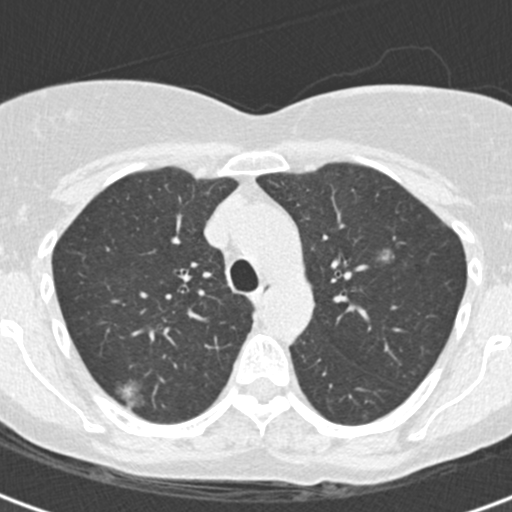
Low-dose screening chest CT, one axial slice. Position 126 of 172 along the scan axis. Lung window (W 1500 / L -600 HU). 2 mm slice thickness. 512 × 512 image matrix, field of view 283 × 283 mm.
Outlined on this slice (manually delineated by an expert):
- lesion 1 (tumor, upper lobe of right lung): box from (x=116, y=379) to (x=145, y=411) px